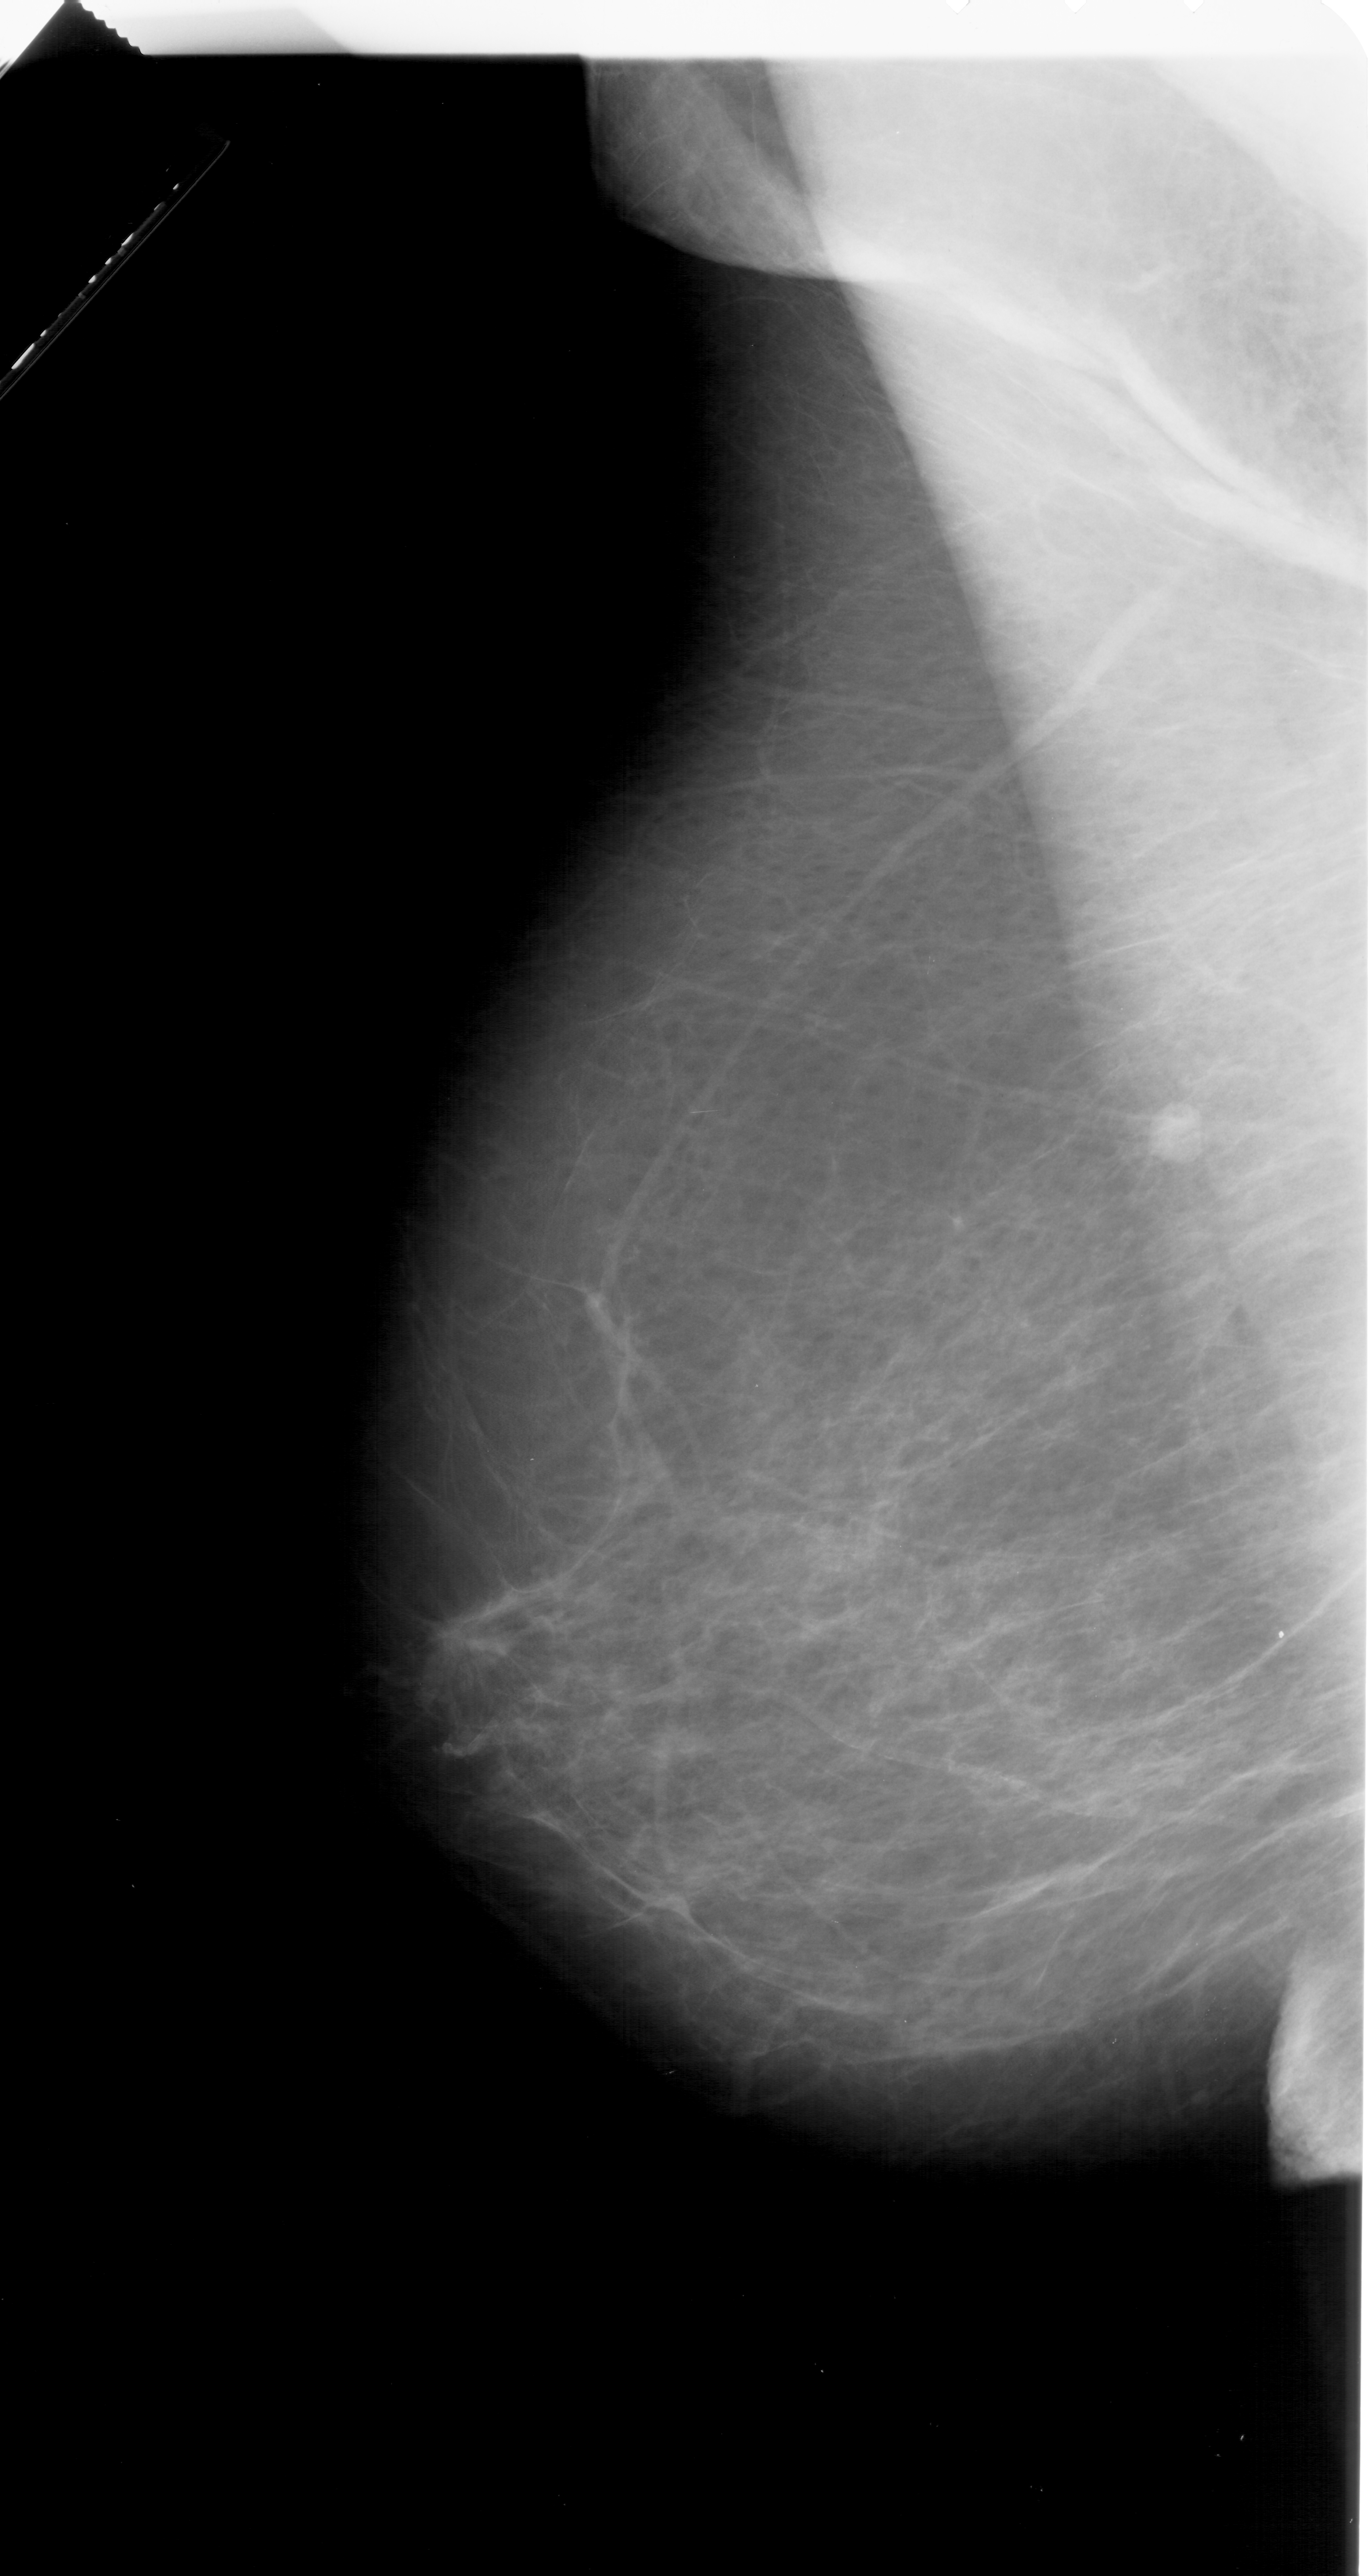
Mammogram (digitized film), left breast, MLO view.
Marked findings (only marked abnormalities are described; nothing is implied about the rest of the image): mass, shape irregular, margins spiculated; BI-RADS assessment category 5; pathology (as recorded): malignant.